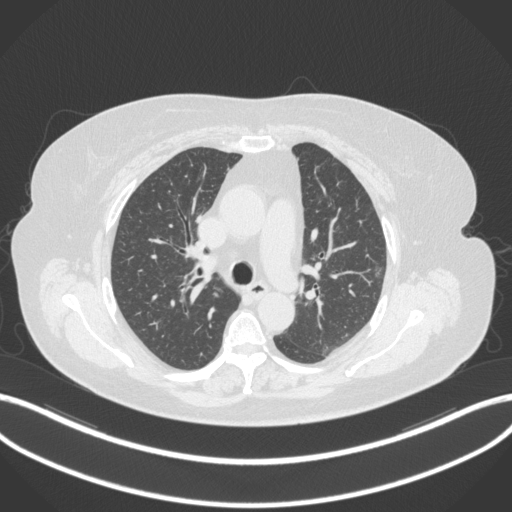
Chest CT, one axial slice; position 212 of 310 along the scan axis; lung window (W 1500 / L -600 HU); 1 mm slice thickness; 512 × 512 image matrix, field of view 400 × 400 mm. Patient: female, 70 years. Case-level facts recorded for this patient, not image findings: clinical TNM (as recorded): T1c N0 M0.
Outlined on this slice (rectangle marked by the reading radiologist):
- lung tumour (recorded histology: adenocarcinoma): bounding box <373,264,384,280> (left, top, right, bottom; pixels)